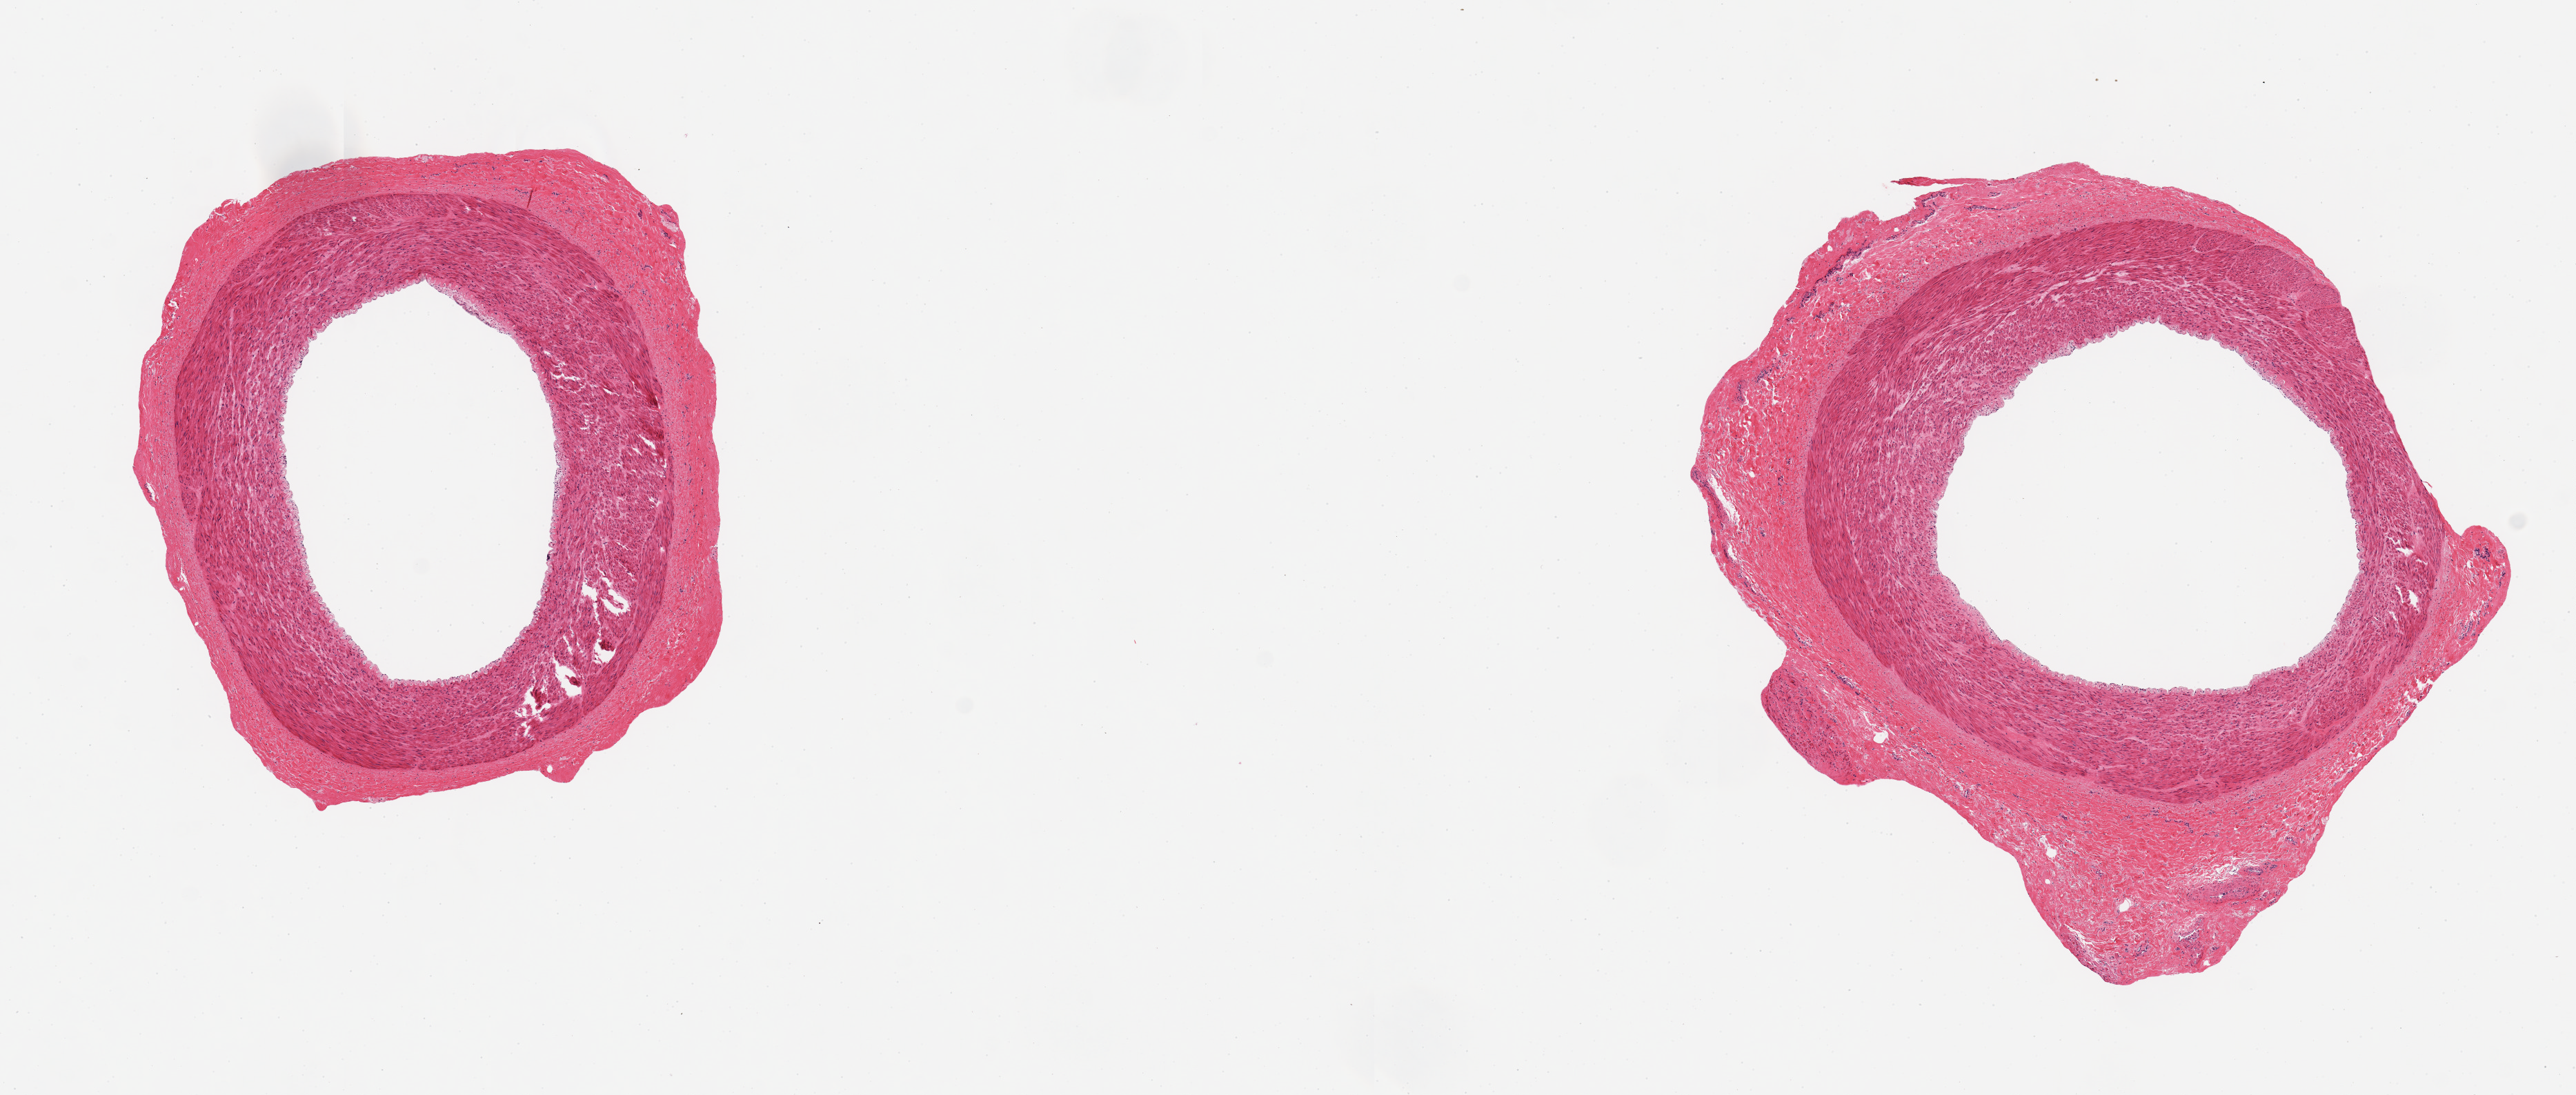
Digitized H&E-stained section — low-resolution overview of the scanned area, about 14.8 x 6.3 mm (acquisition: 20x scan). PAXgene-fixed paraffin-embedded (PFPE) section. Section of tibial artery (target tissue). Tissue donor sample. Male donor.
Pathologist's review note for this sample: 2 pieces, excellent clean specimen.